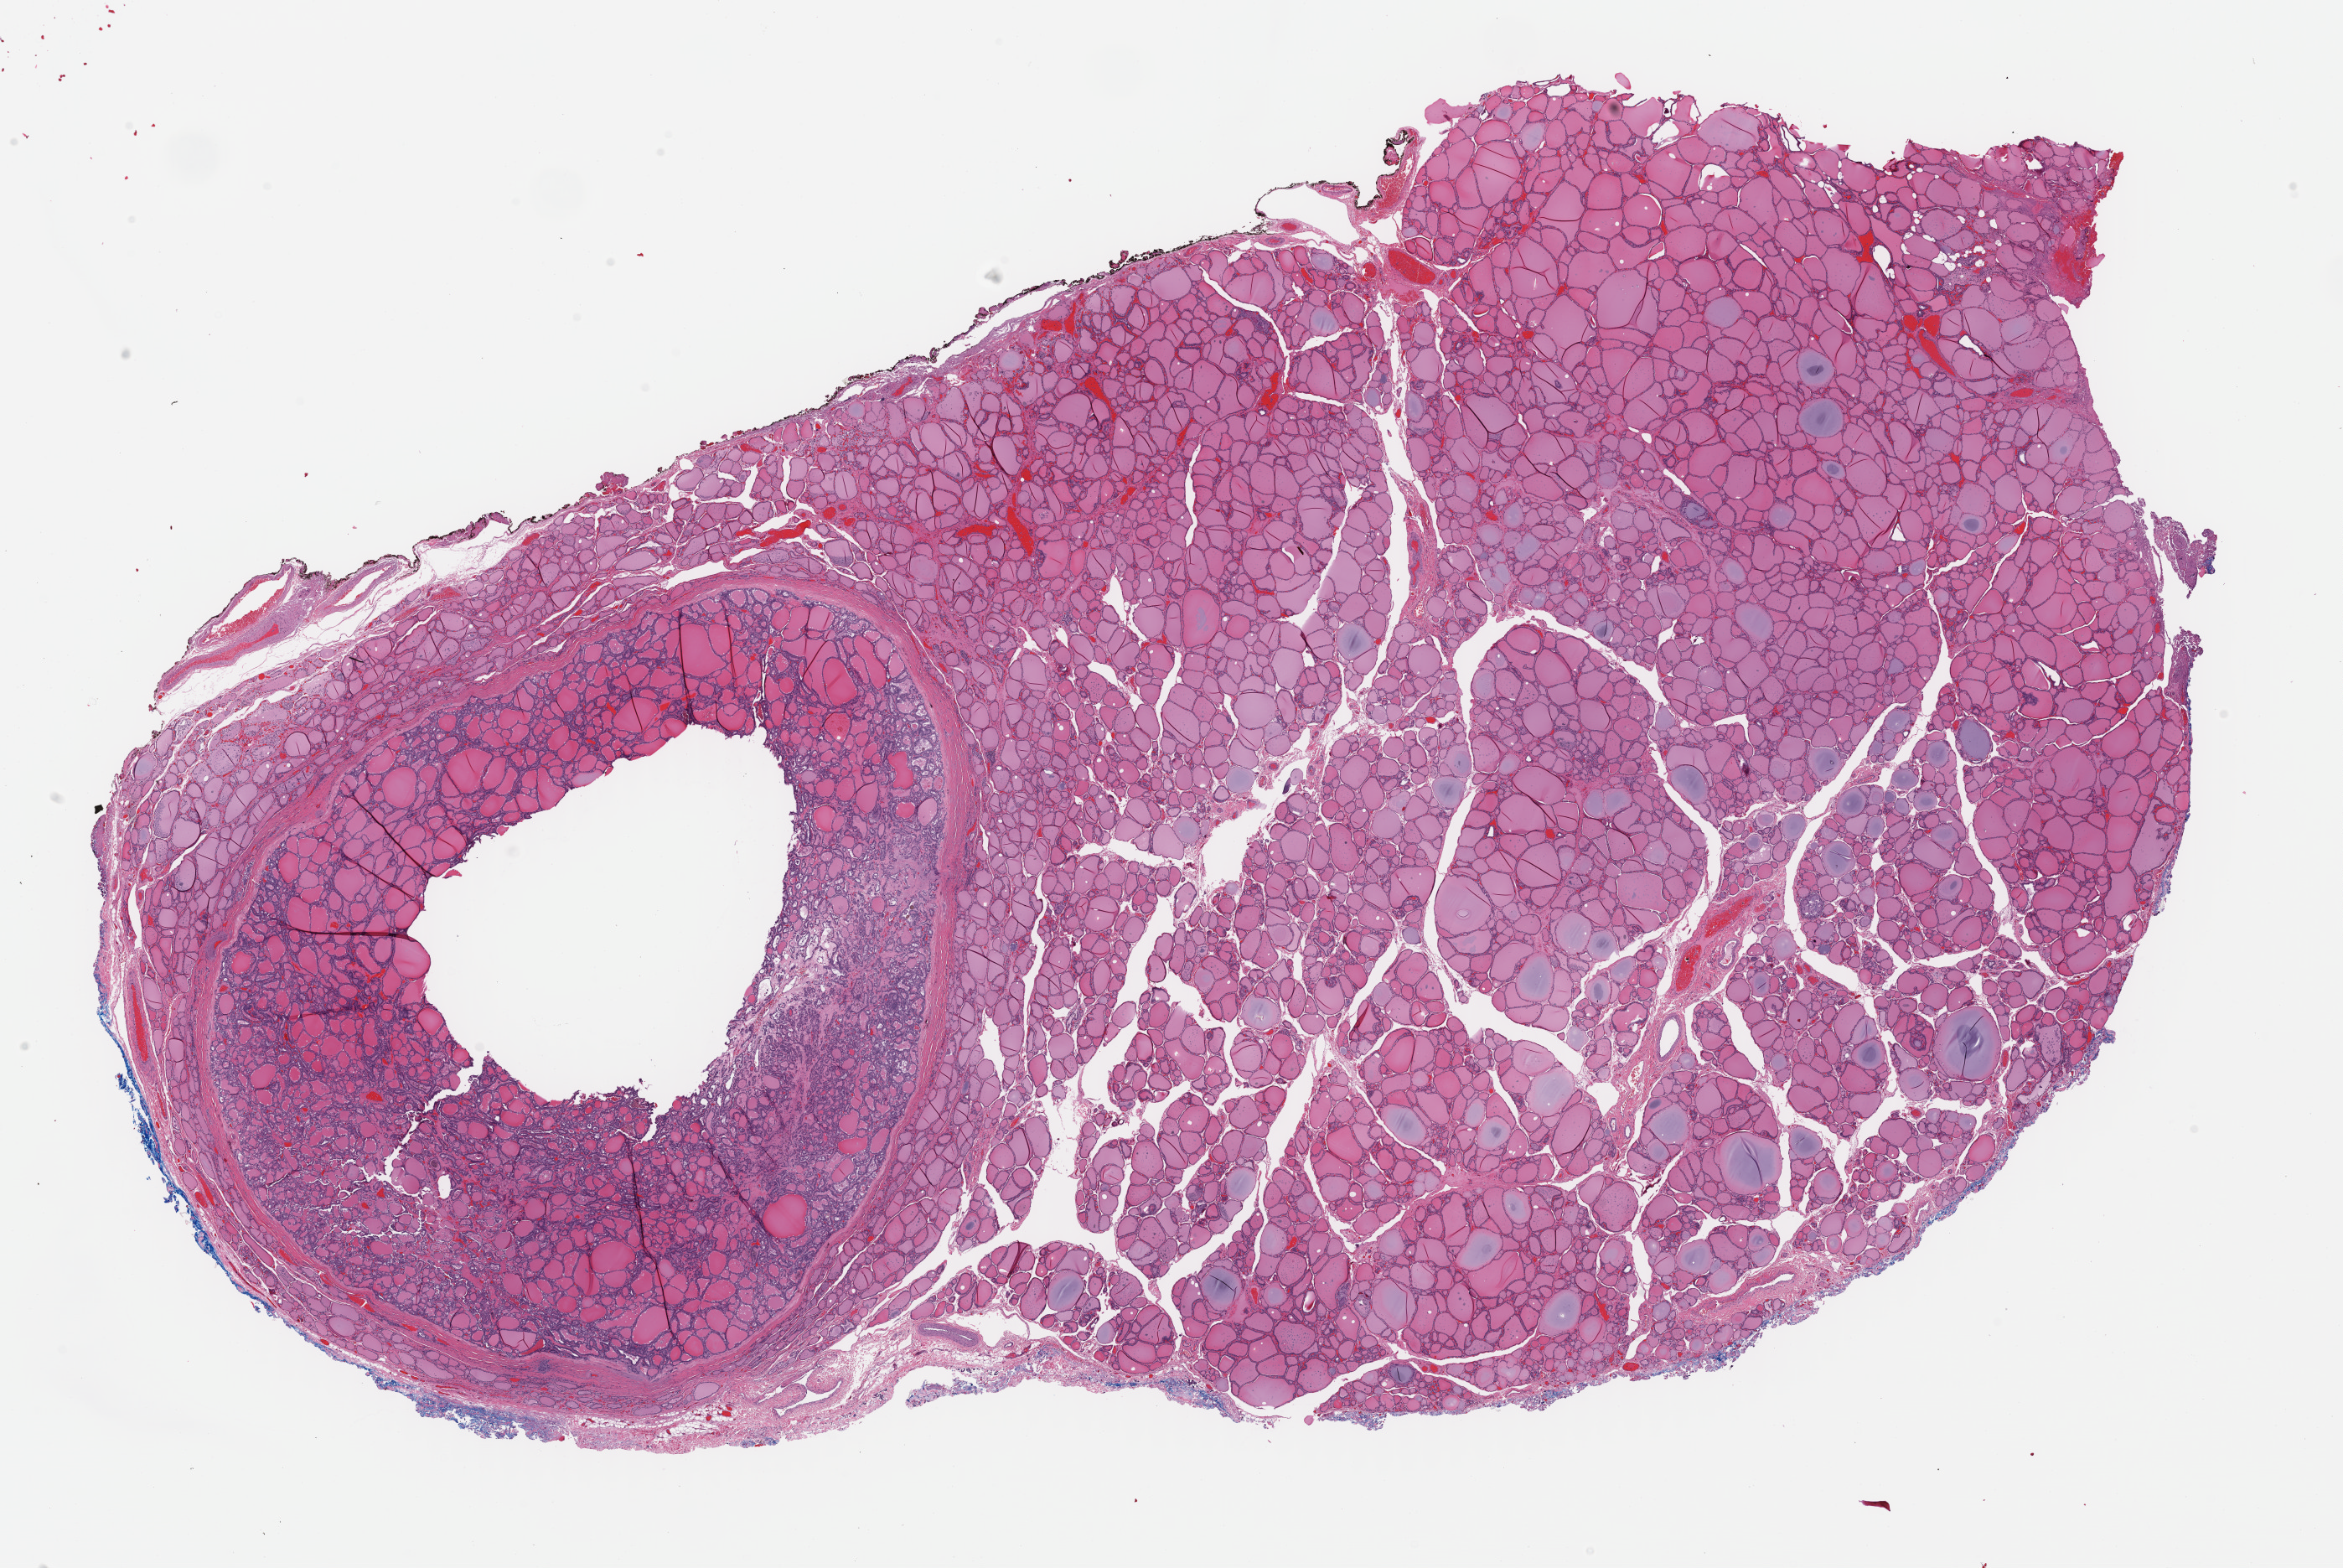
Whole-slide histology image, H&E-stained — low-resolution overview of the scanned area, about 22.1 x 14.8 mm (acquisition: 40x scan), formalin-fixed paraffin-embedded (FFPE) diagnostic section, sample: primary tumour, thyroid. Female patient; age at initial diagnosis 51 years.
* AJCC pathologic stage: III (7th edition)
* diagnosis: Papillary carcinoma, follicular variant (thyroid gland)
* lymph nodes positive (case pathology): 4 of 7 examined